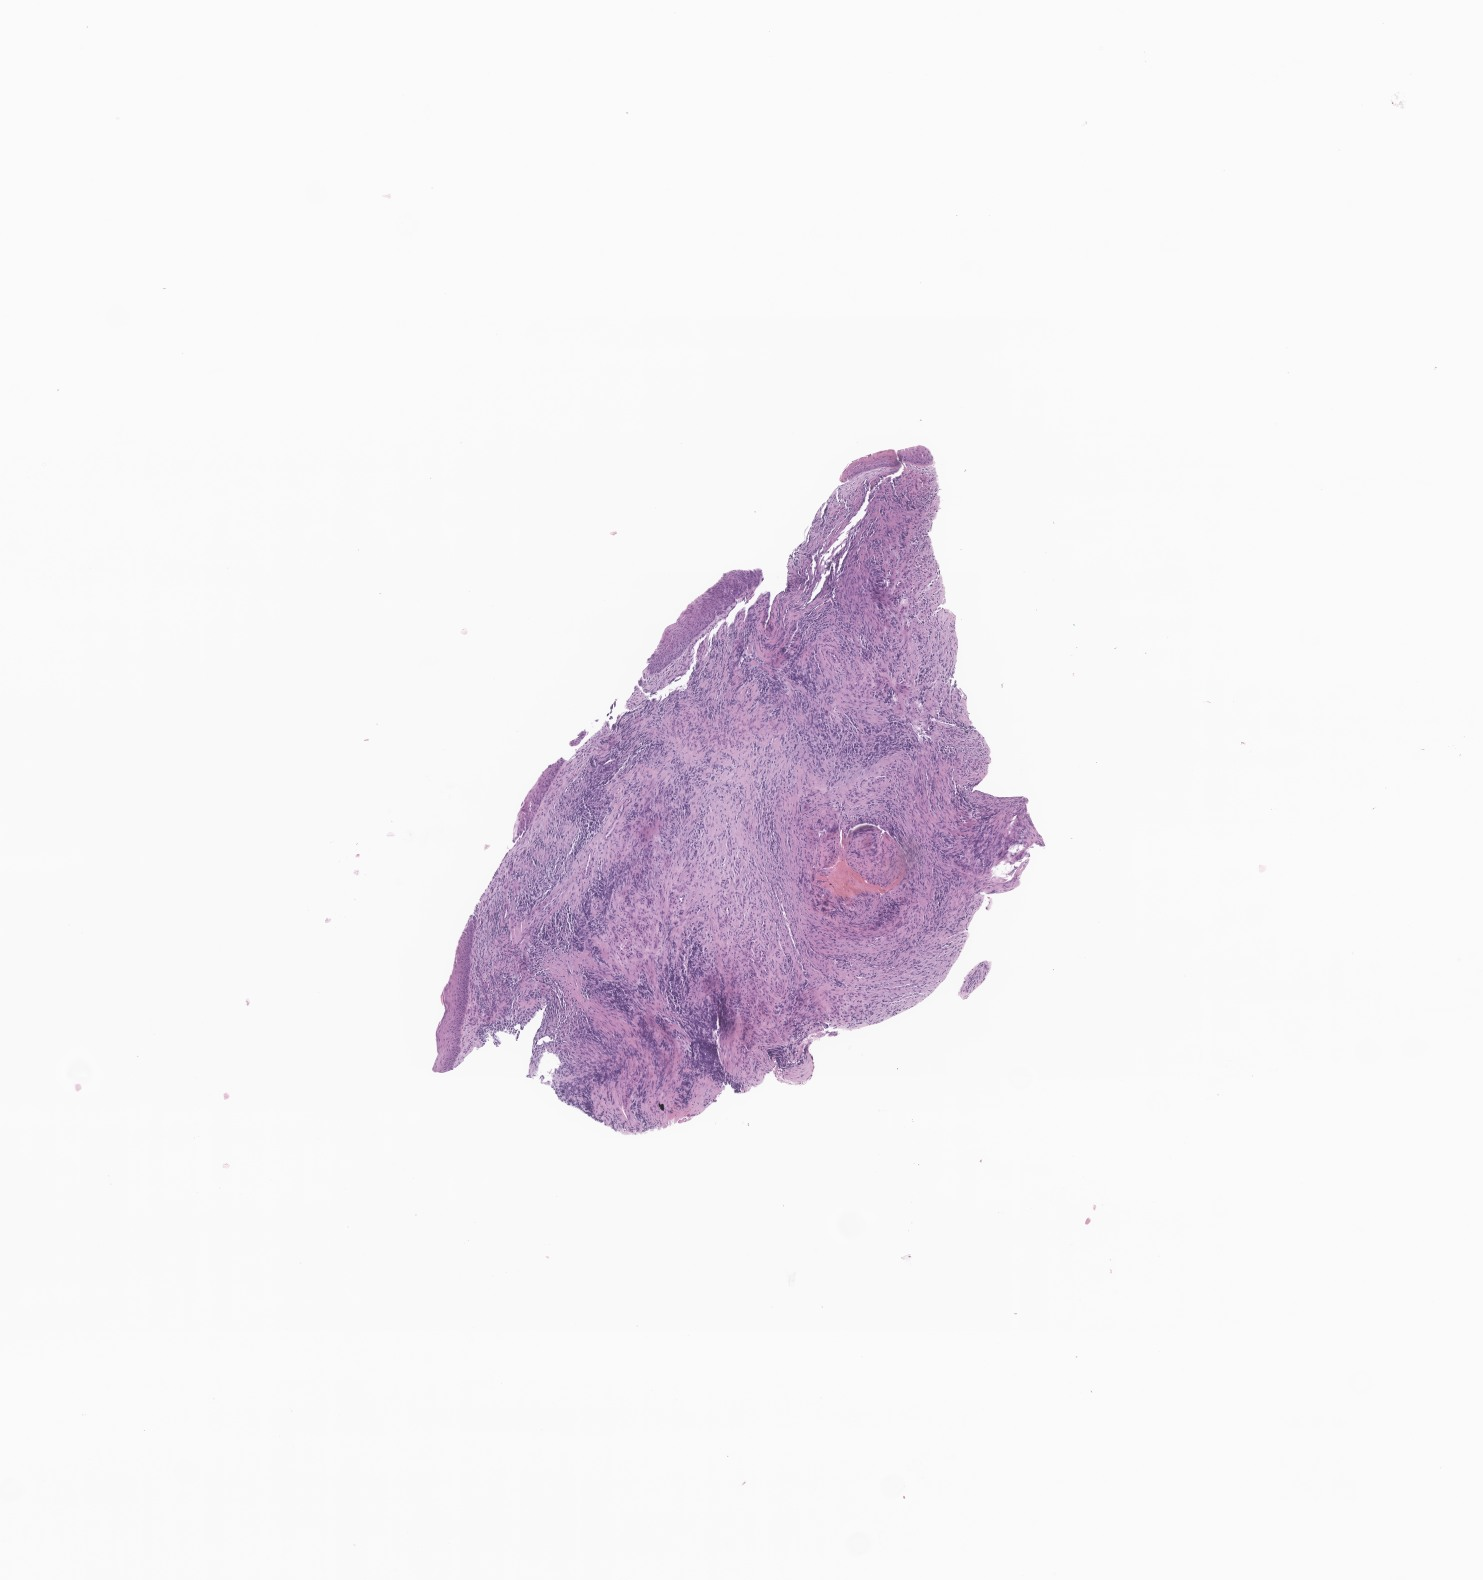
Haematoxylin and eosin whole-slide image of tumor tissue from the head and neck — low-resolution overview of the scanned area, about 6.3 x 6.7 mm, formalin-fixed, paraffin-embedded (FFPE) tissue. Patient: male, age 45 months.
Recorded diagnosis: Embryonal rhabdomyosarcoma, NOS.